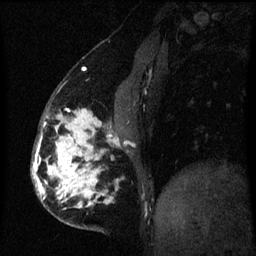
Breast MRI (dynamic contrast-enhanced), one sagittal slice. Slice 21 of 60 in the series (ordered by position). Dynamic contrast-enhanced series, image 2 of 3 at this slice position (ordered by acquisition). 1.5 T. TE 4.2 ms, TR 8 ms. 2 mm slice thickness. 256 × 256 image matrix, field of view 190 × 190 mm. Patient: female, 50 years.
Structures marked on this image (semi-automatic segmentation, software-assisted and operator-edited):
- analysis volume of interest (the breast-tissue region the enhancement analysis was run in; not a lesion): box from (x=32, y=110) to (x=120, y=229) px
- tumour enhancement mask (voxels above the 70 % enhancement threshold inside the analysis volume of interest): (x=32, y=110)–(x=116, y=209)